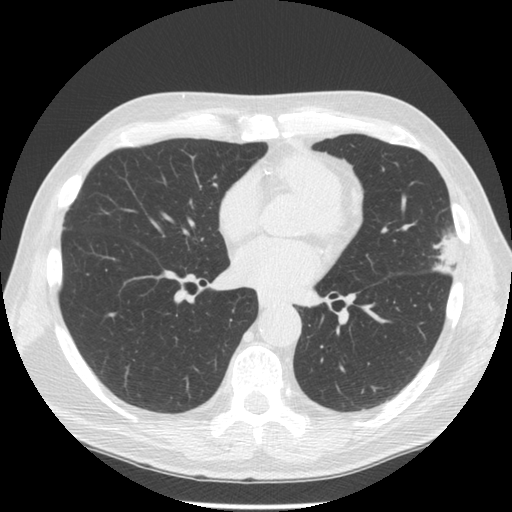
Low-dose screening chest CT, one axial slice. Slice 66 of 134 in the series (ordered by position). Reconstruction kernel STANDARD. Lung window (W 1500 / L -600 HU). 2.5 mm slice thickness. 512 × 512 image matrix.
Outlined on this slice (expert manual segmentation):
- lesion 1 (tumor, upper lobe of left lung): bounding box [x1, y1, x2, y2] px = [433, 234, 460, 274]